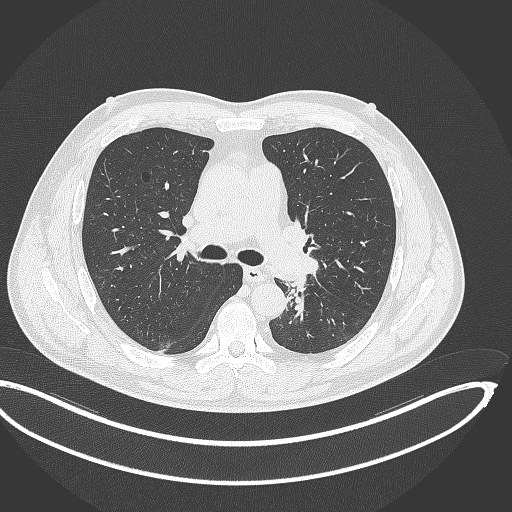
Chest CT, one axial slice; slice 220 of 362 in the series (ordered by position); 120 kVp; lung window (W 1500 / L -600 HU); 1 mm slice thickness; 512 × 512 image matrix, field of view 442 × 442 mm. Patient: male, 50 years. Case-level facts recorded for this patient, not image findings: clinical TNM (as recorded): T2a N3 M0.
Annotated regions visible in this slice (bounding box drawn by a radiologist):
- lung tumour (recorded histology: squamous cell carcinoma): bounding box (x1, y1, x2, y2) in pixels: (283, 274, 308, 322)